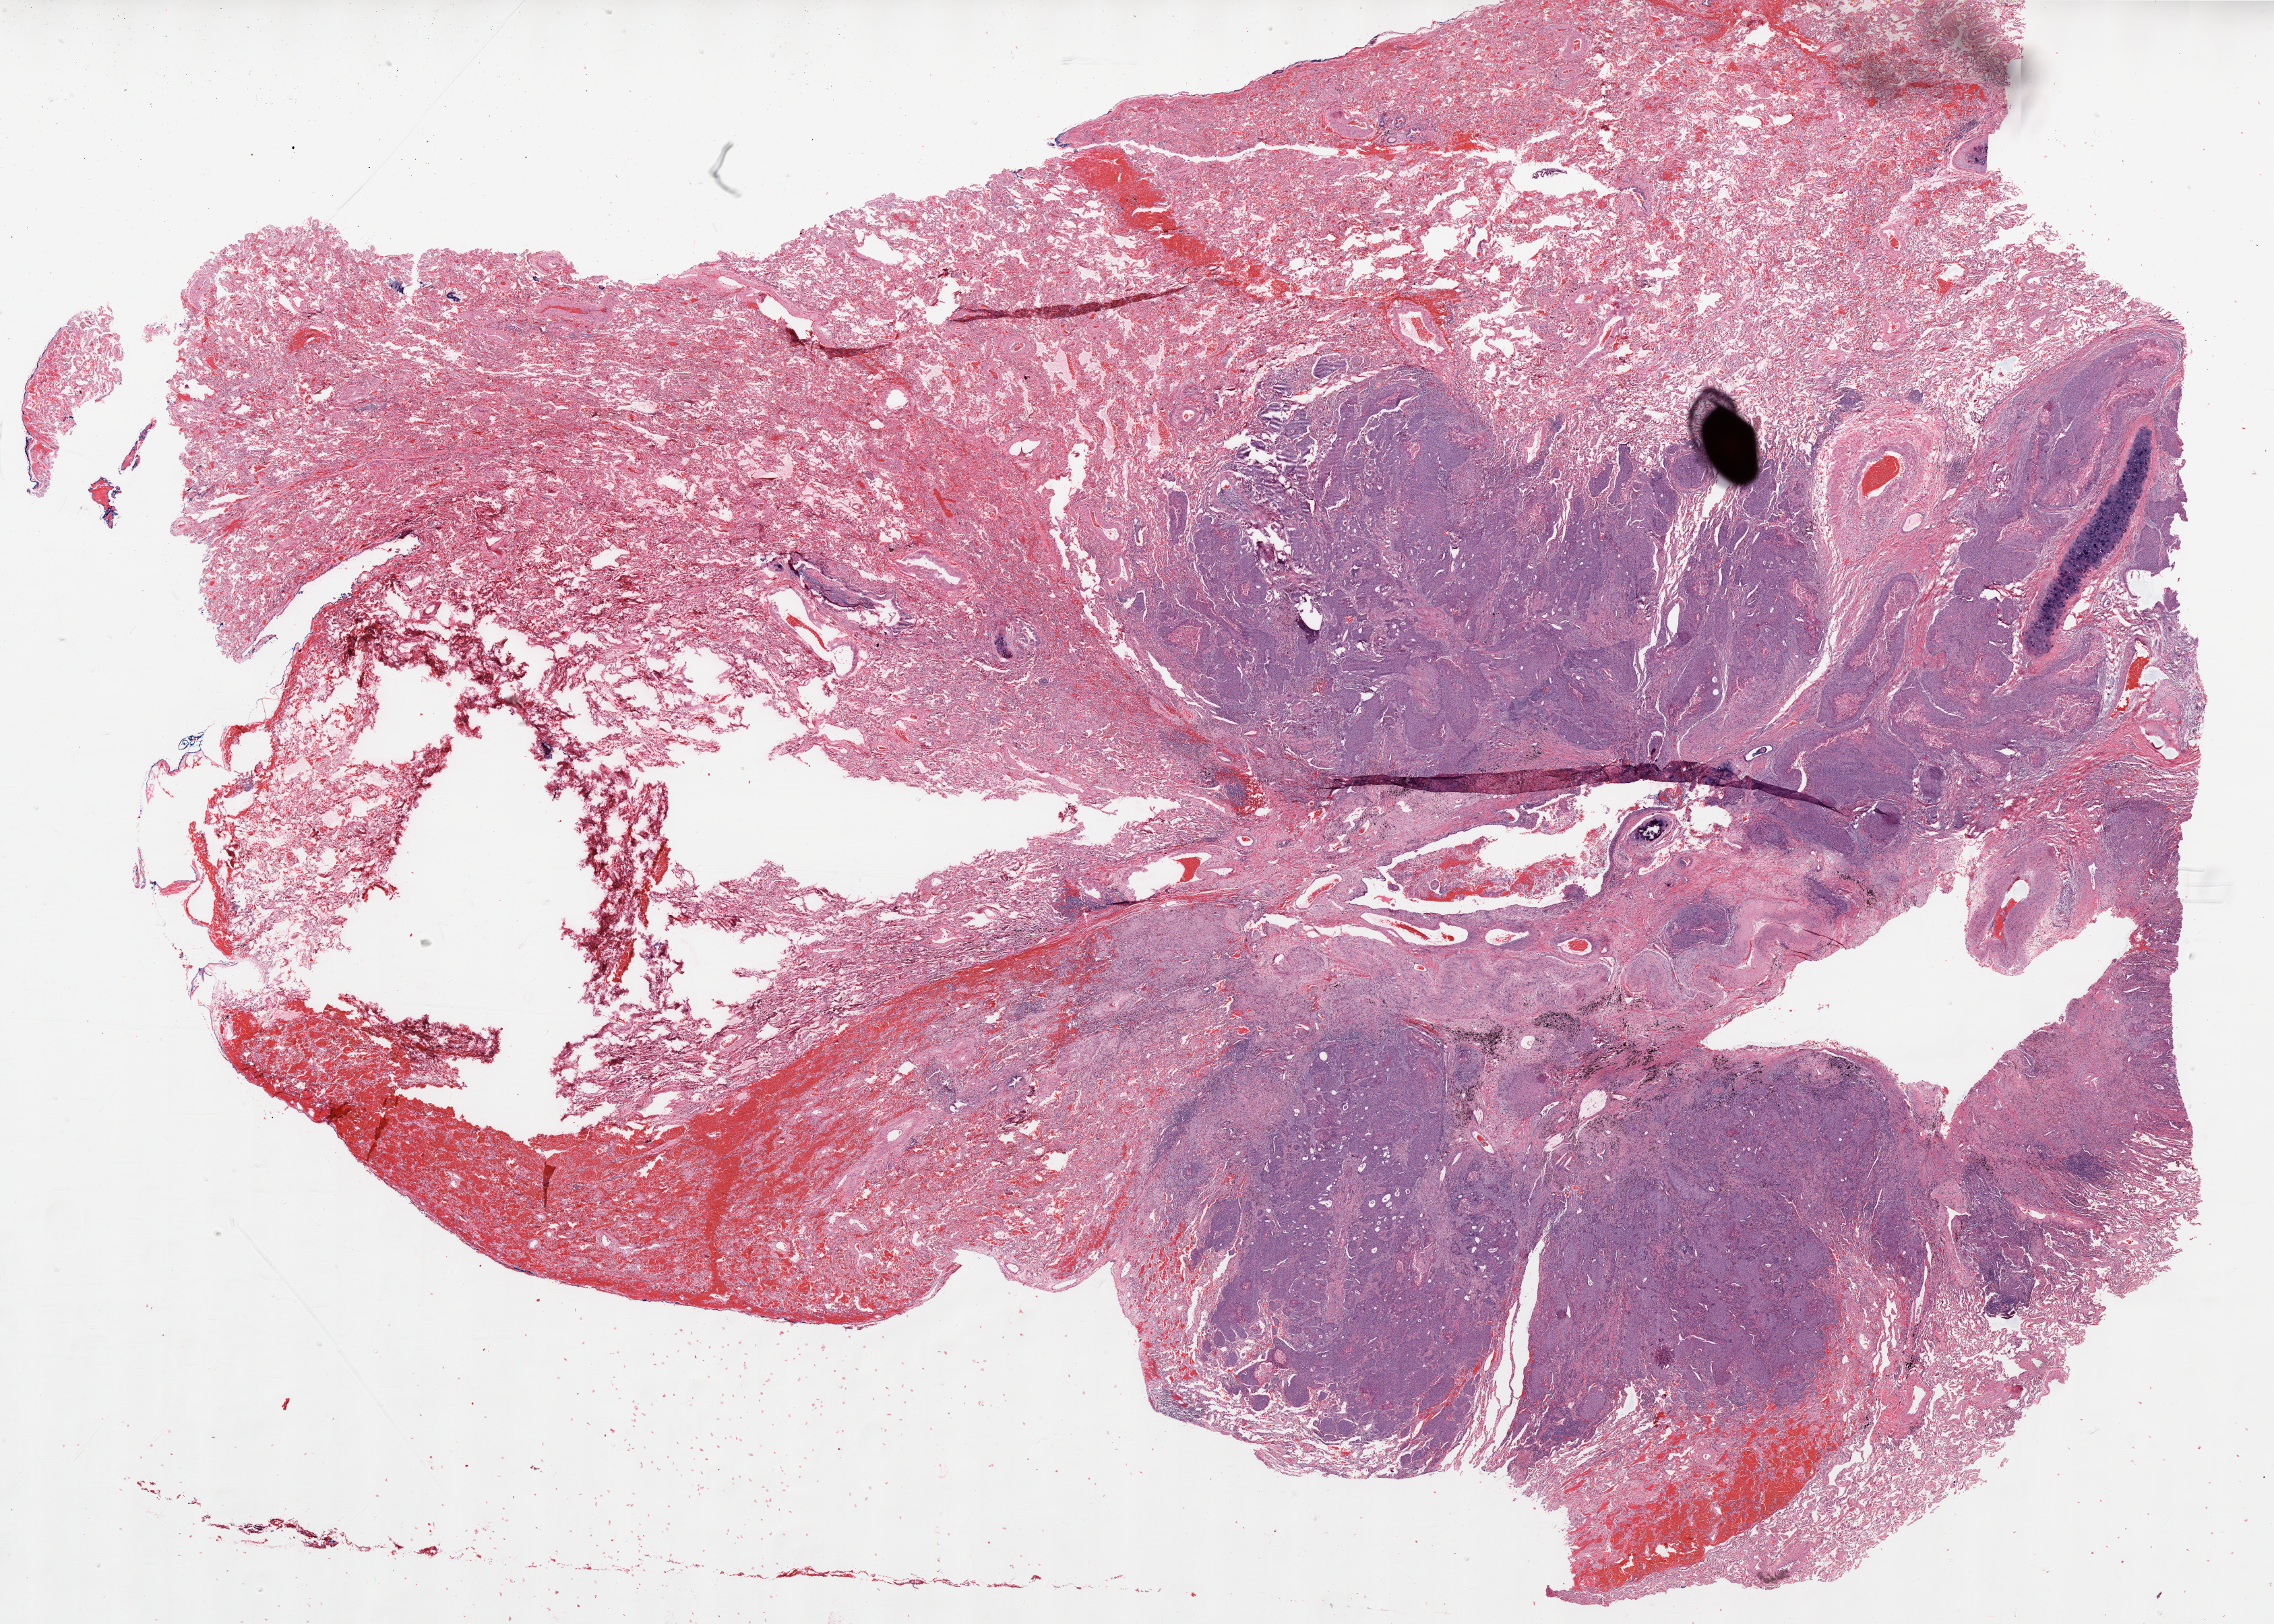
Digitized H&E tissue section (whole slide) — shown as a low-resolution overview of the whole scanned area (about 27.1 x 19.4 mm, slide scanned at 20x); formalin-fixed paraffin-embedded (FFPE) diagnostic section; lung, primary tumour sample. Patient: female, age at initial diagnosis 67 years.
* TNM: T1 N1 M0
* diagnosis: Squamous cell carcinoma, NOS (upper lobe, lung)
* AJCC pathologic stage: IIA (6th edition)